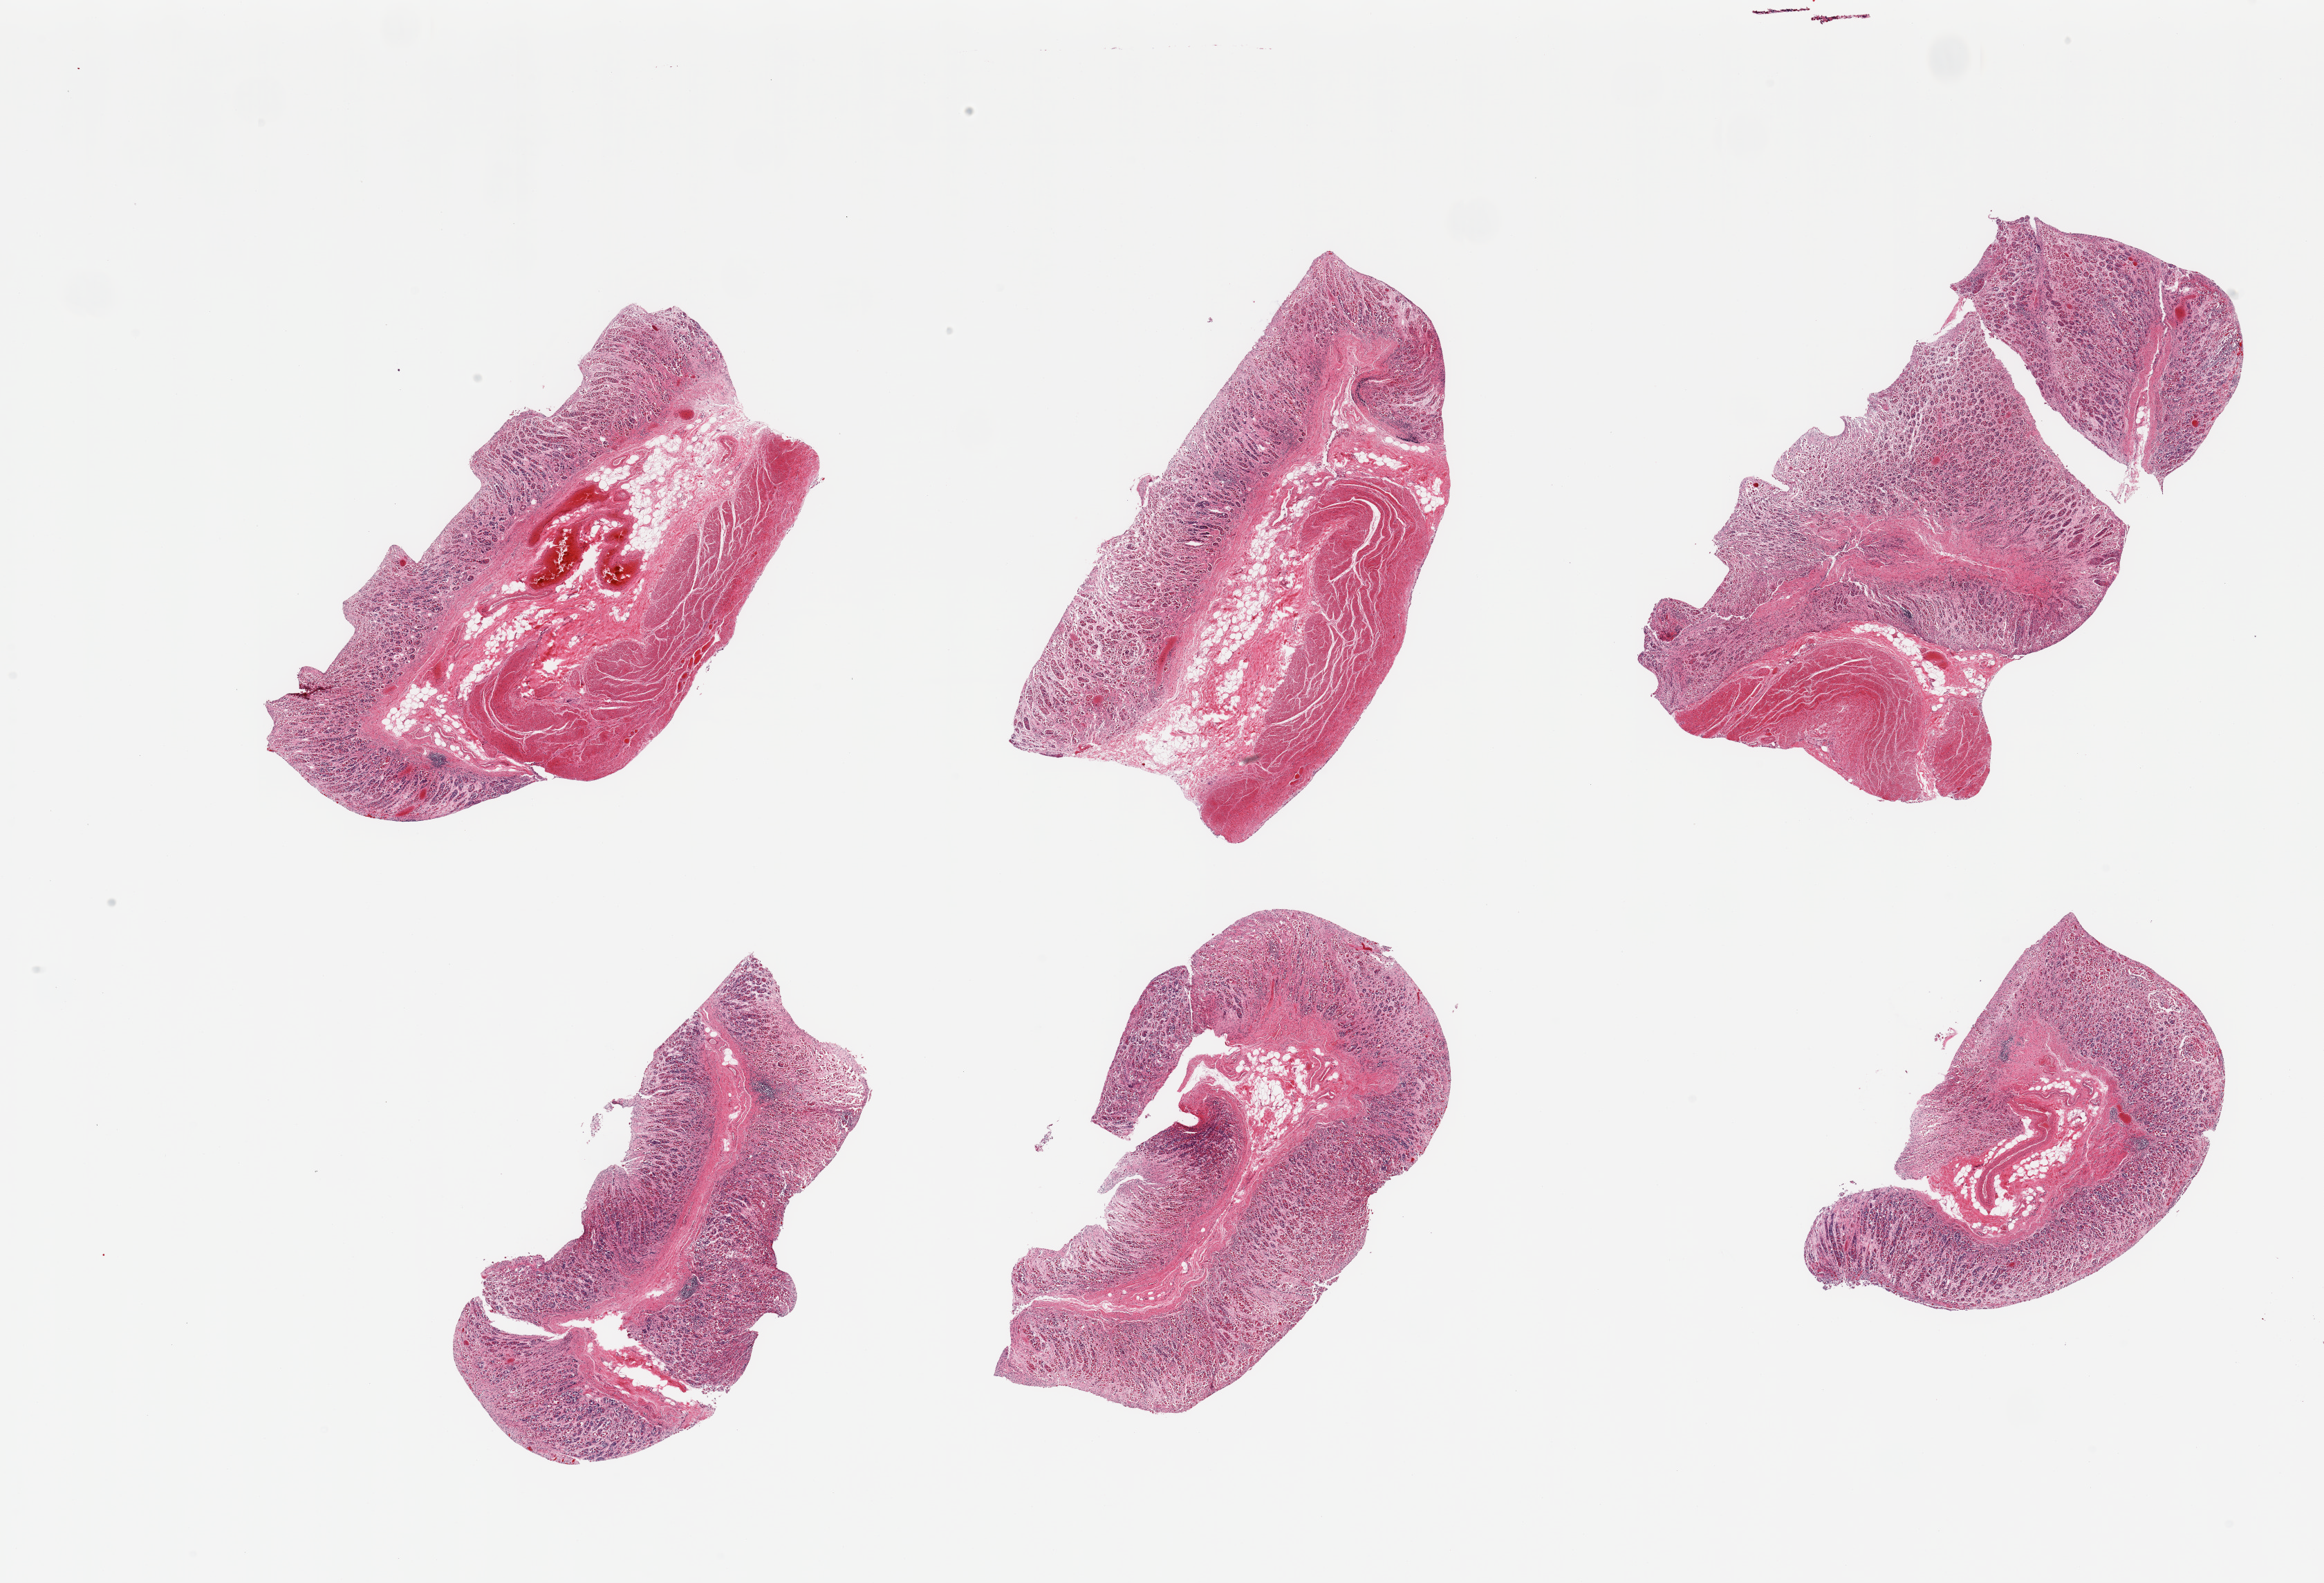
Whole-slide image, haematoxylin and eosin stain, brightfield — low-resolution overview of the scanned area, about 26.6 x 18.1 mm, PAXgene-fixed, paraffin-embedded tissue, target tissue: stomach, tissue donor sample. Male donor.
* pathologist's review note for this sample: 6 pieces, mucosa up to ~1.2mm, near-total autolysis